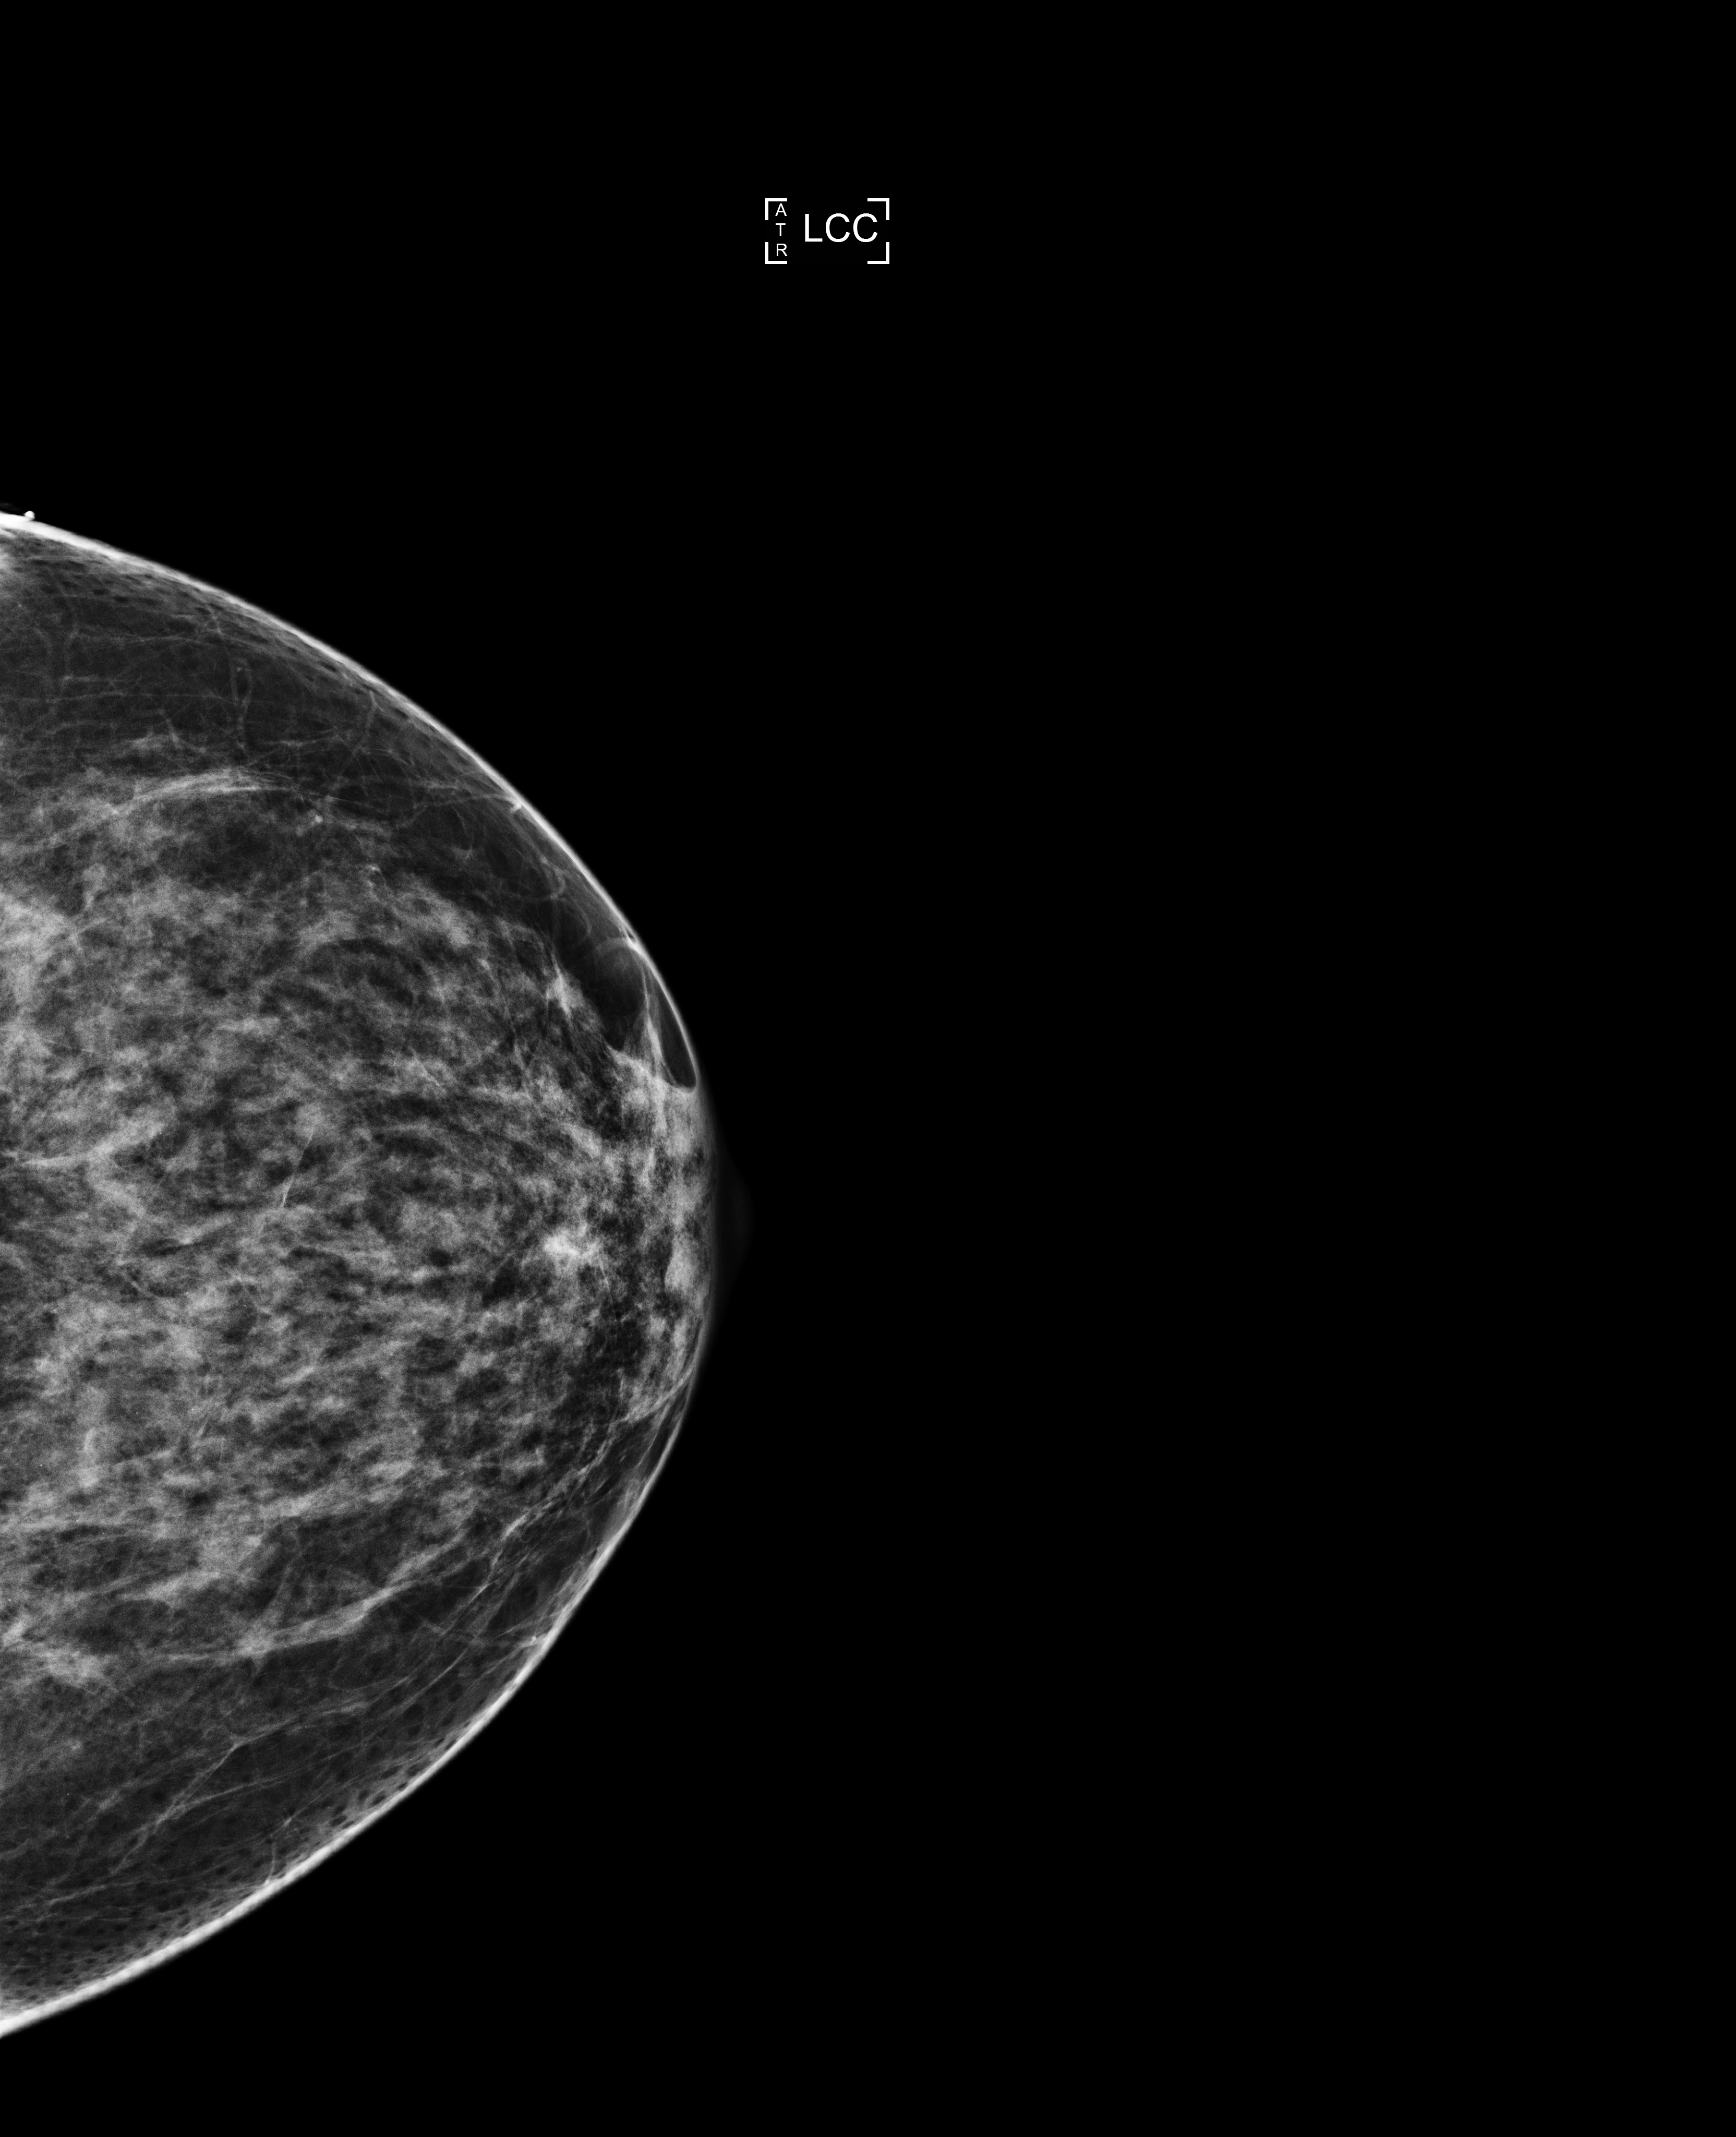
Annual screening mammography examination; compressed breast thickness 67 mm. Patient aged 53 years (female).
Image type: full-field digital mammogram. Breast: left. Projection: CC view.